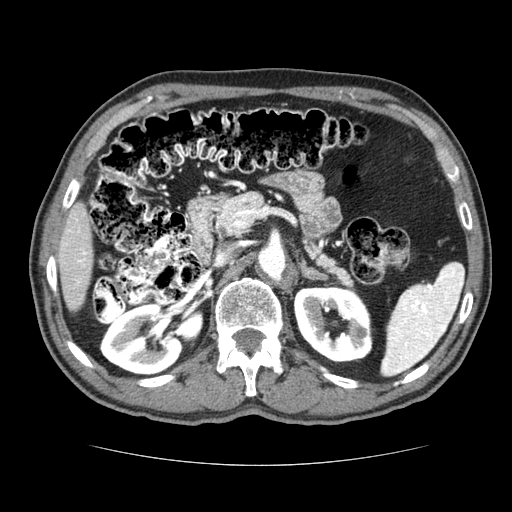
Contrast-enhanced abdominal CT (liver protocol), one axial slice. Slice 33 of 79 in the series (ordered by position). Reconstruction kernel STANDARD. 120 kVp. Soft-tissue window (W 400 / L 40 HU). 2.5 mm slice thickness. 512 × 512 image matrix, field of view 360 × 360 mm. From the clinical record (not read from this slice): diagnosis: hepatocellular carcinoma (patient treated with transarterial chemoembolisation; whether this scan precedes or follows treatment is not stated here); TNM stage (as recorded): Stage-I; Child-Pugh class: A; tumour nodularity: uninodular.
Outlined on this slice (semi-automatic segmentation, software-assisted and operator-edited):
- liver parenchyma outside the tumour (the mass and vessels are separate outlines, so this box may not span the whole liver): bounding box [x1, y1, x2, y2] px = [56, 202, 92, 312]
- liver vessels: [65, 218, 87, 285]